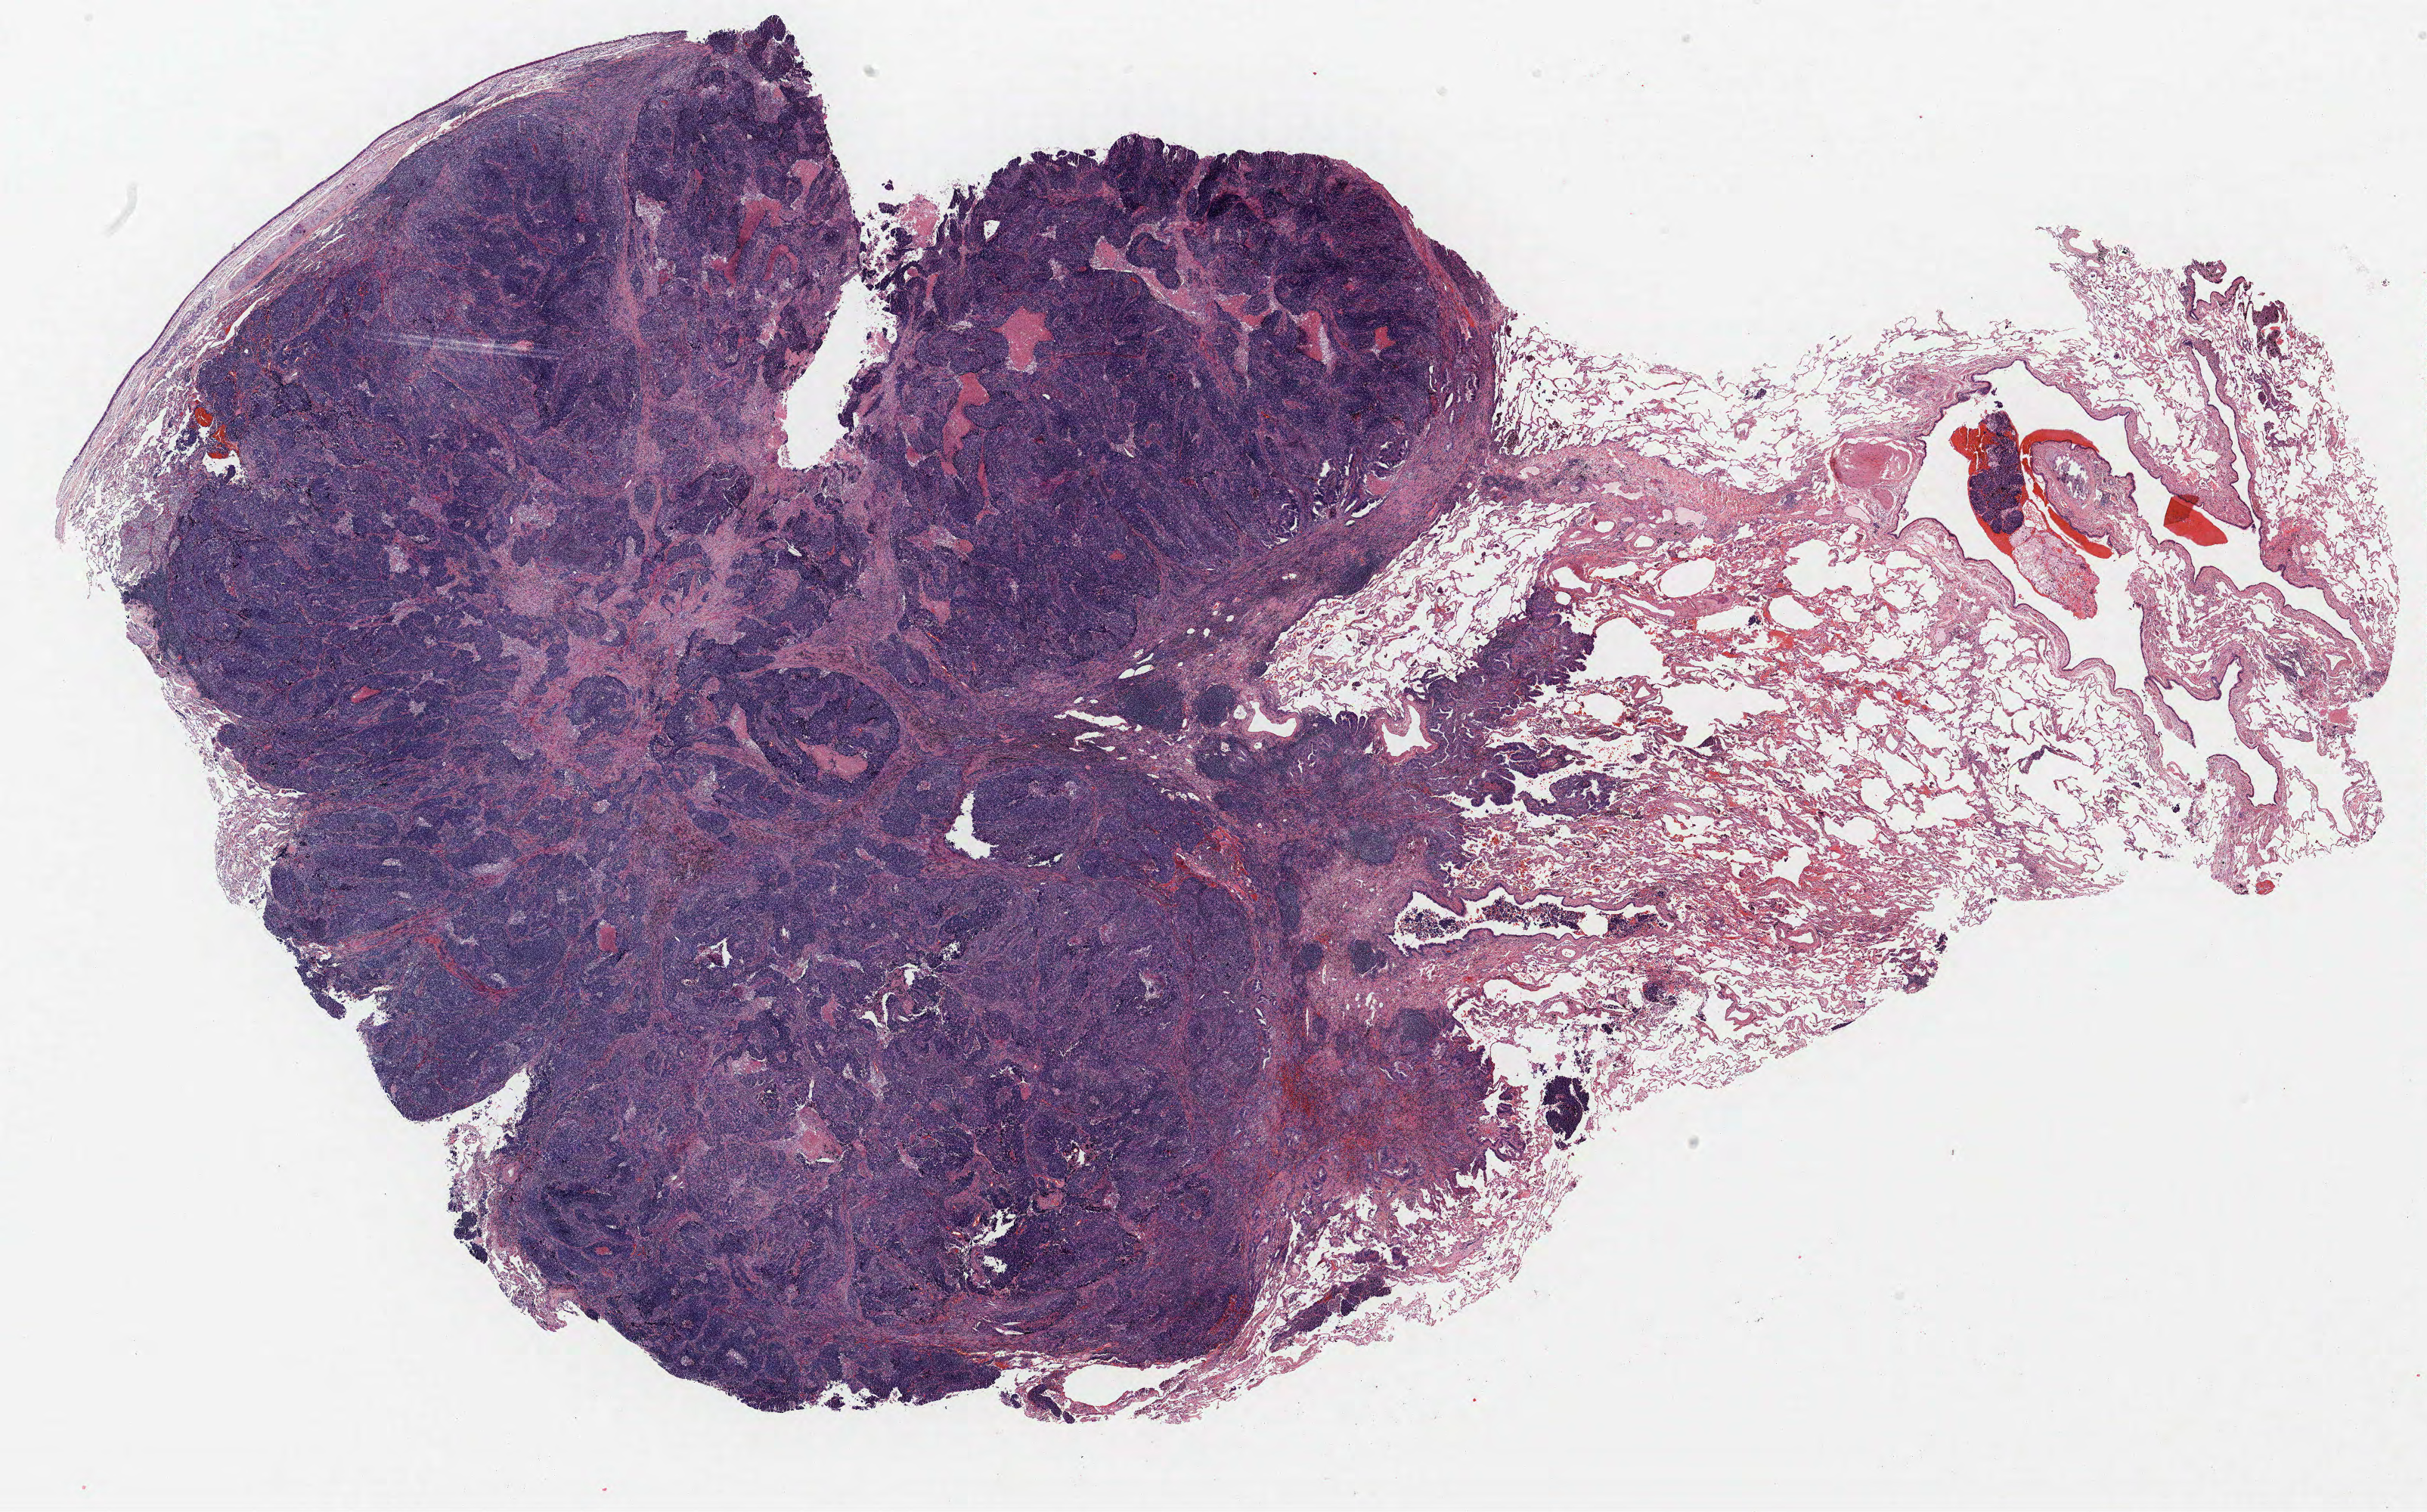
H&E whole-slide image — a low-resolution overview of the entire scanned area, about 25.7 x 16.0 mm (acquisition: 40x scan), FFPE section, lung. Male patient, aged 67 at enrolment. Grade: poorly differentiated (G3).
Participant's lung-cancer diagnosis: Adenocarcinoma, NOS (ICD-O-3 8140/3). Stage (AJCC 6th edition): IIA. Tumour size (pathology): 18 mm. Primary tumour location (clinical record): left upper lobe, left lower lobe.